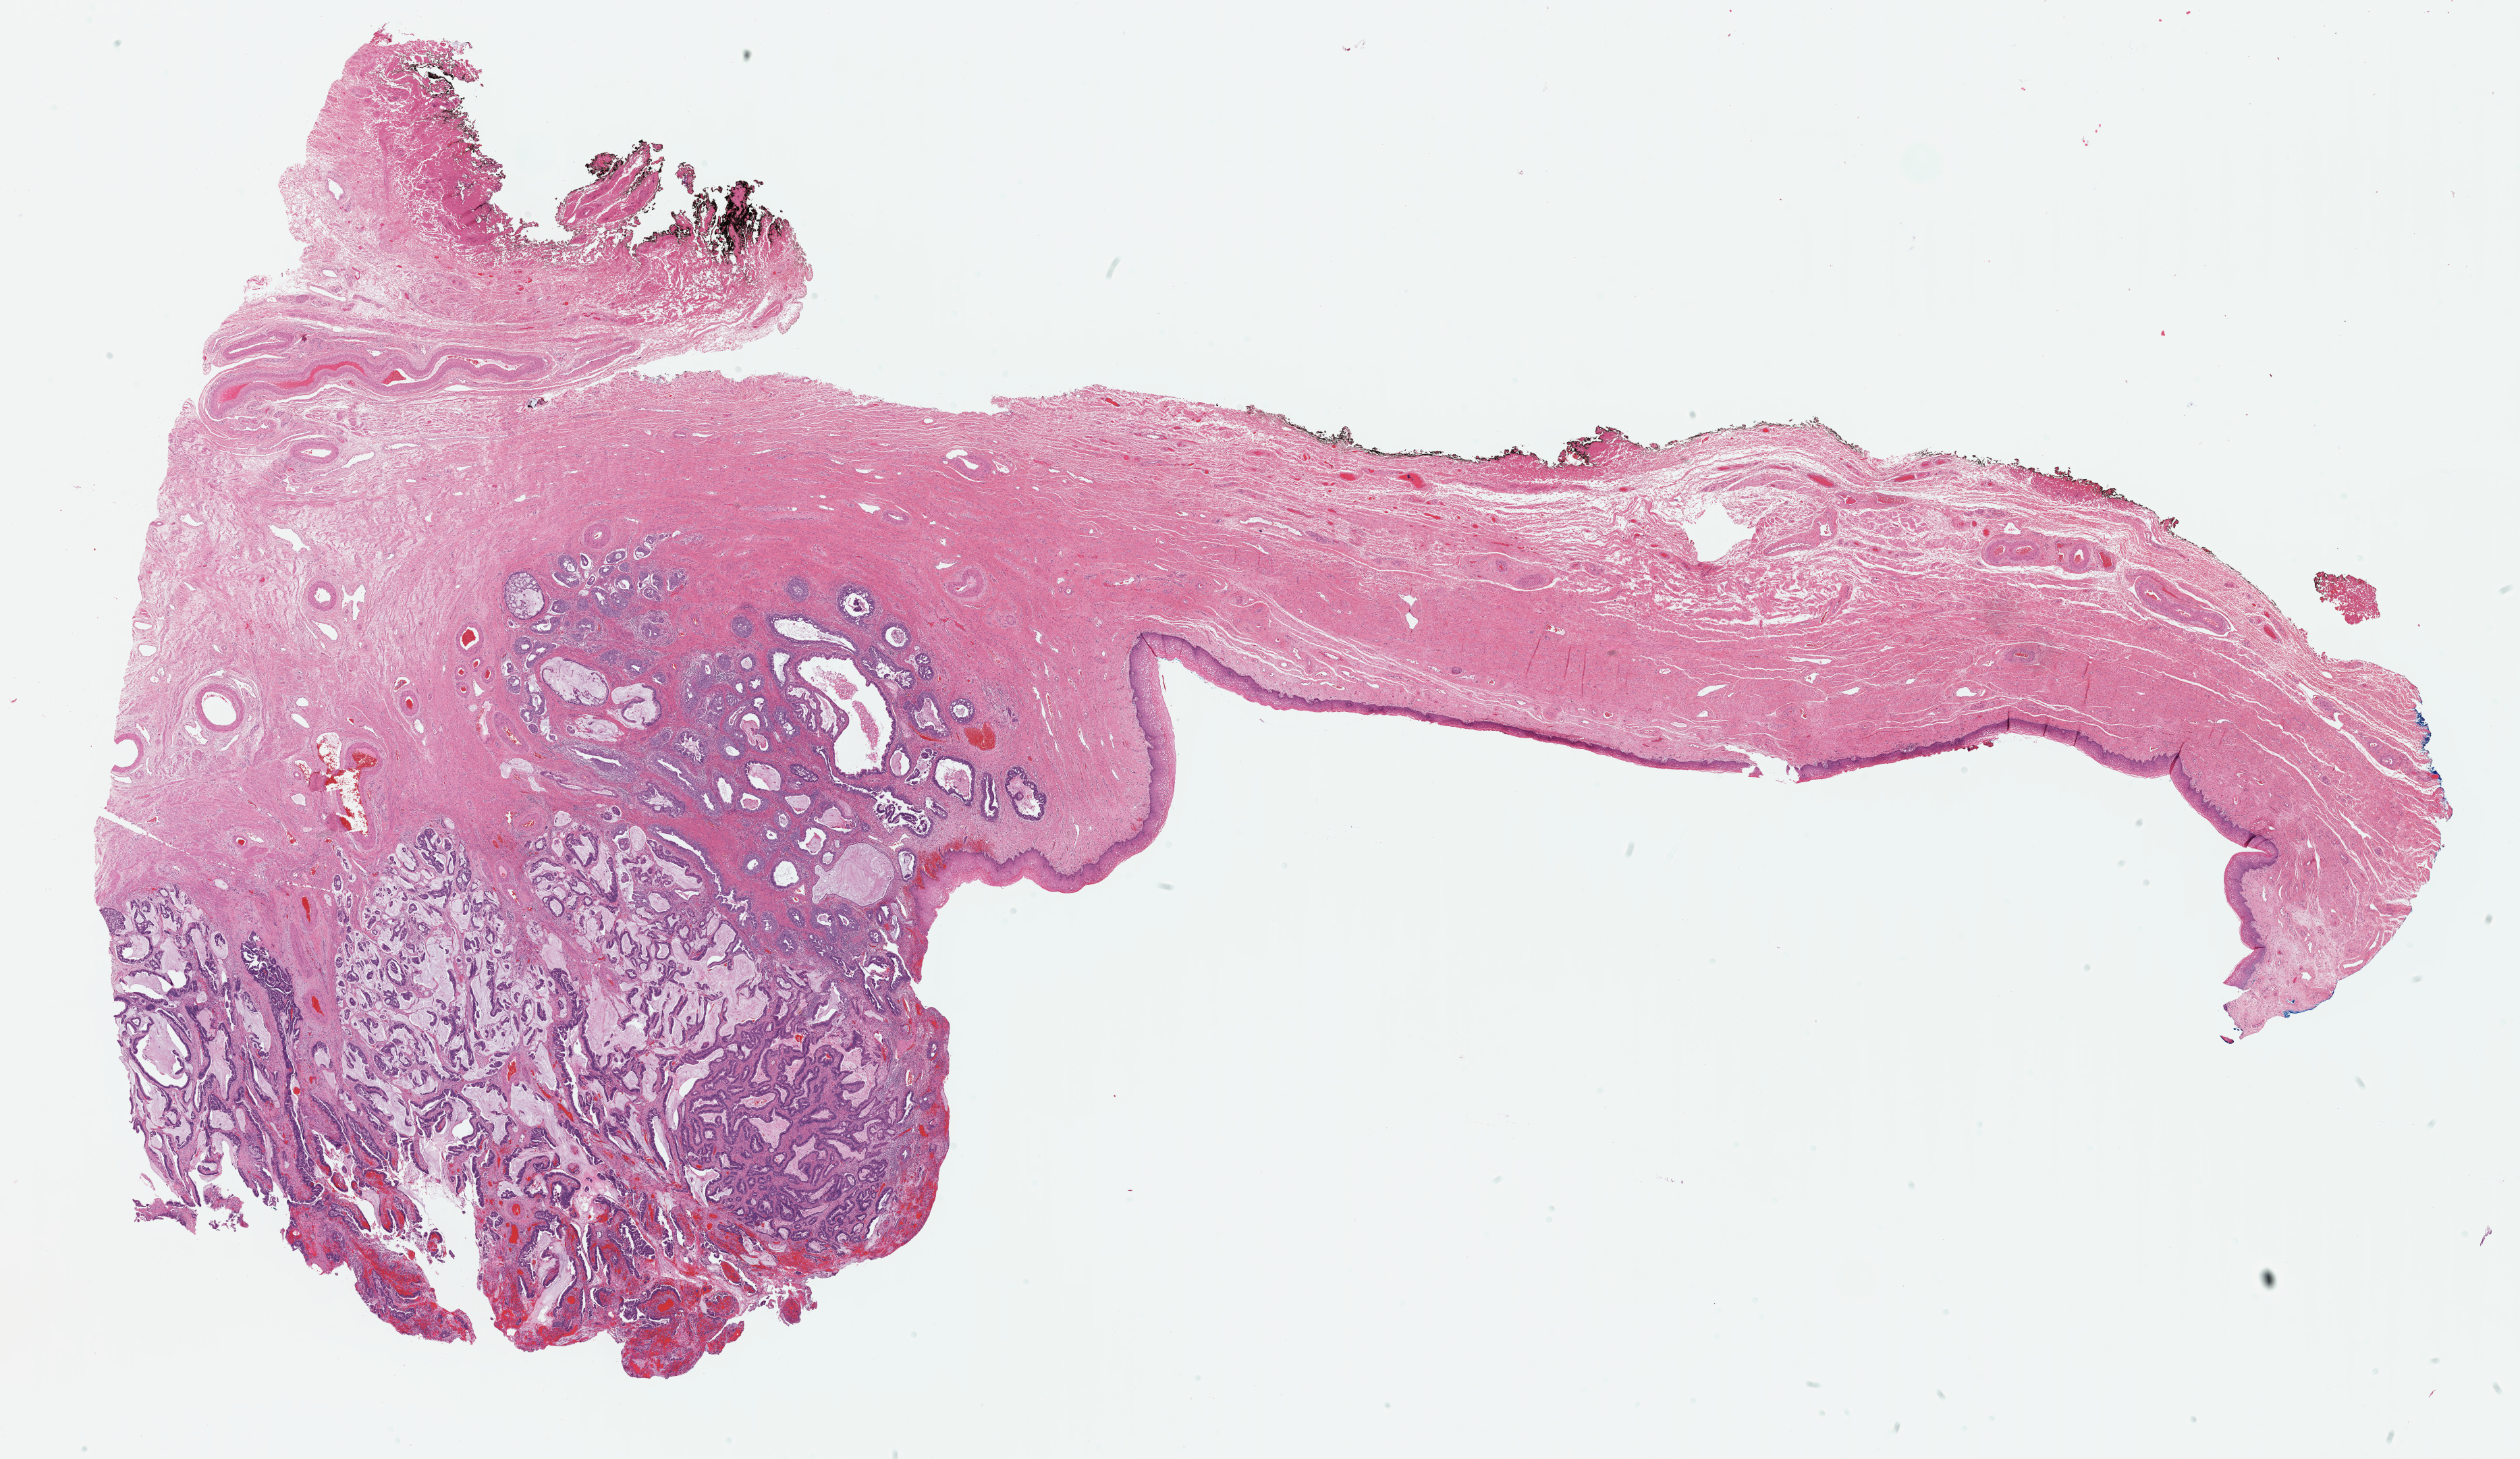
Whole-slide histology image, H&E-stained, shown as a low-resolution overview of the whole scanned area (about 30.2 x 17.5 mm). Formalin-fixed paraffin-embedded (FFPE) diagnostic section. Primary tumour sample from the cervix. Female patient; age at initial diagnosis 34 years. Histologic grade: G2 (moderately differentiated).
• lymph nodes positive (case pathology): 0 of 22 examined
• histologic diagnosis: Mucinous adenocarcinoma (cervix uteri)
• FIGO stage: IB1